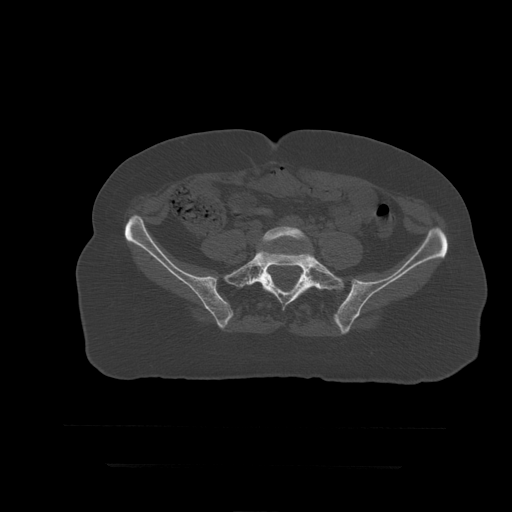
CT including the spine, one axial slice; reconstruction kernel STANDARD; 120 kVp; bone window (W 1800 / L 400 HU); 1.25 mm slice thickness; 512 × 512 image matrix, field of view 450 × 450 mm. Patient age 41 years. From the clinical record (not read from this slice): primary cancer: breast.
Outlined on this slice (semi-automatic segmentation, software-assisted and operator-edited):
- L5 vertebra: bounding box [x1, y1, x2, y2] px = [261, 227, 313, 252]